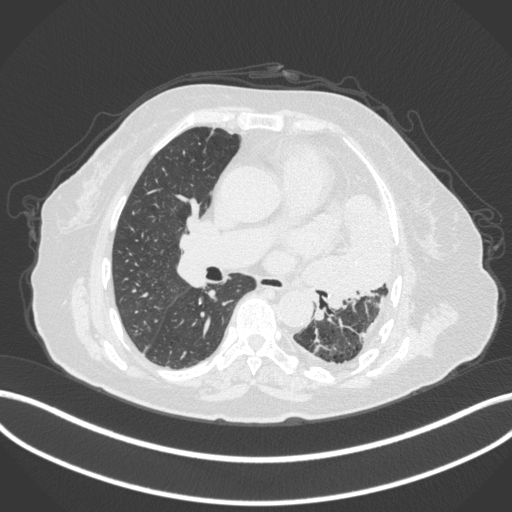
Chest CT, one axial slice; slice 198 of 399 in the series (ordered by position); 120 kVp; lung window (W 1500 / L -600 HU); 1 mm slice thickness; 512 × 512 image matrix, field of view 400 × 400 mm. Female patient, age 75 years. From the clinical record (not read from this slice): clinical TNM (as recorded): T3 N3 M1.
Structures marked on this image (rectangle marked by the reading radiologist):
- lung tumour (recorded histology: adenocarcinoma): bounding box <309,188,398,310> (left, top, right, bottom; pixels)